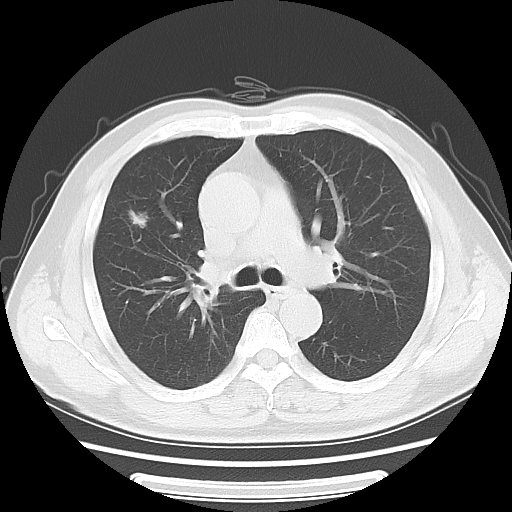
Chest CT, one axial slice. Slice 38 of 63 in the series (ordered by position). Reconstruction kernel LUNG. 120 kVp. Lung window (W 1500 / L -600 HU). 512 × 512 image matrix, field of view 360 × 360 mm. Male patient, age 63 years. From the clinical record (not read from this slice): clinical TNM (as recorded): T1c N0 M0; histopathological grade: G2-3.
Annotated regions visible in this slice (rectangle marked by the reading radiologist):
- lung tumour (recorded histology: adenocarcinoma): bounding box (x1, y1, x2, y2) in pixels: (124, 198, 154, 239)